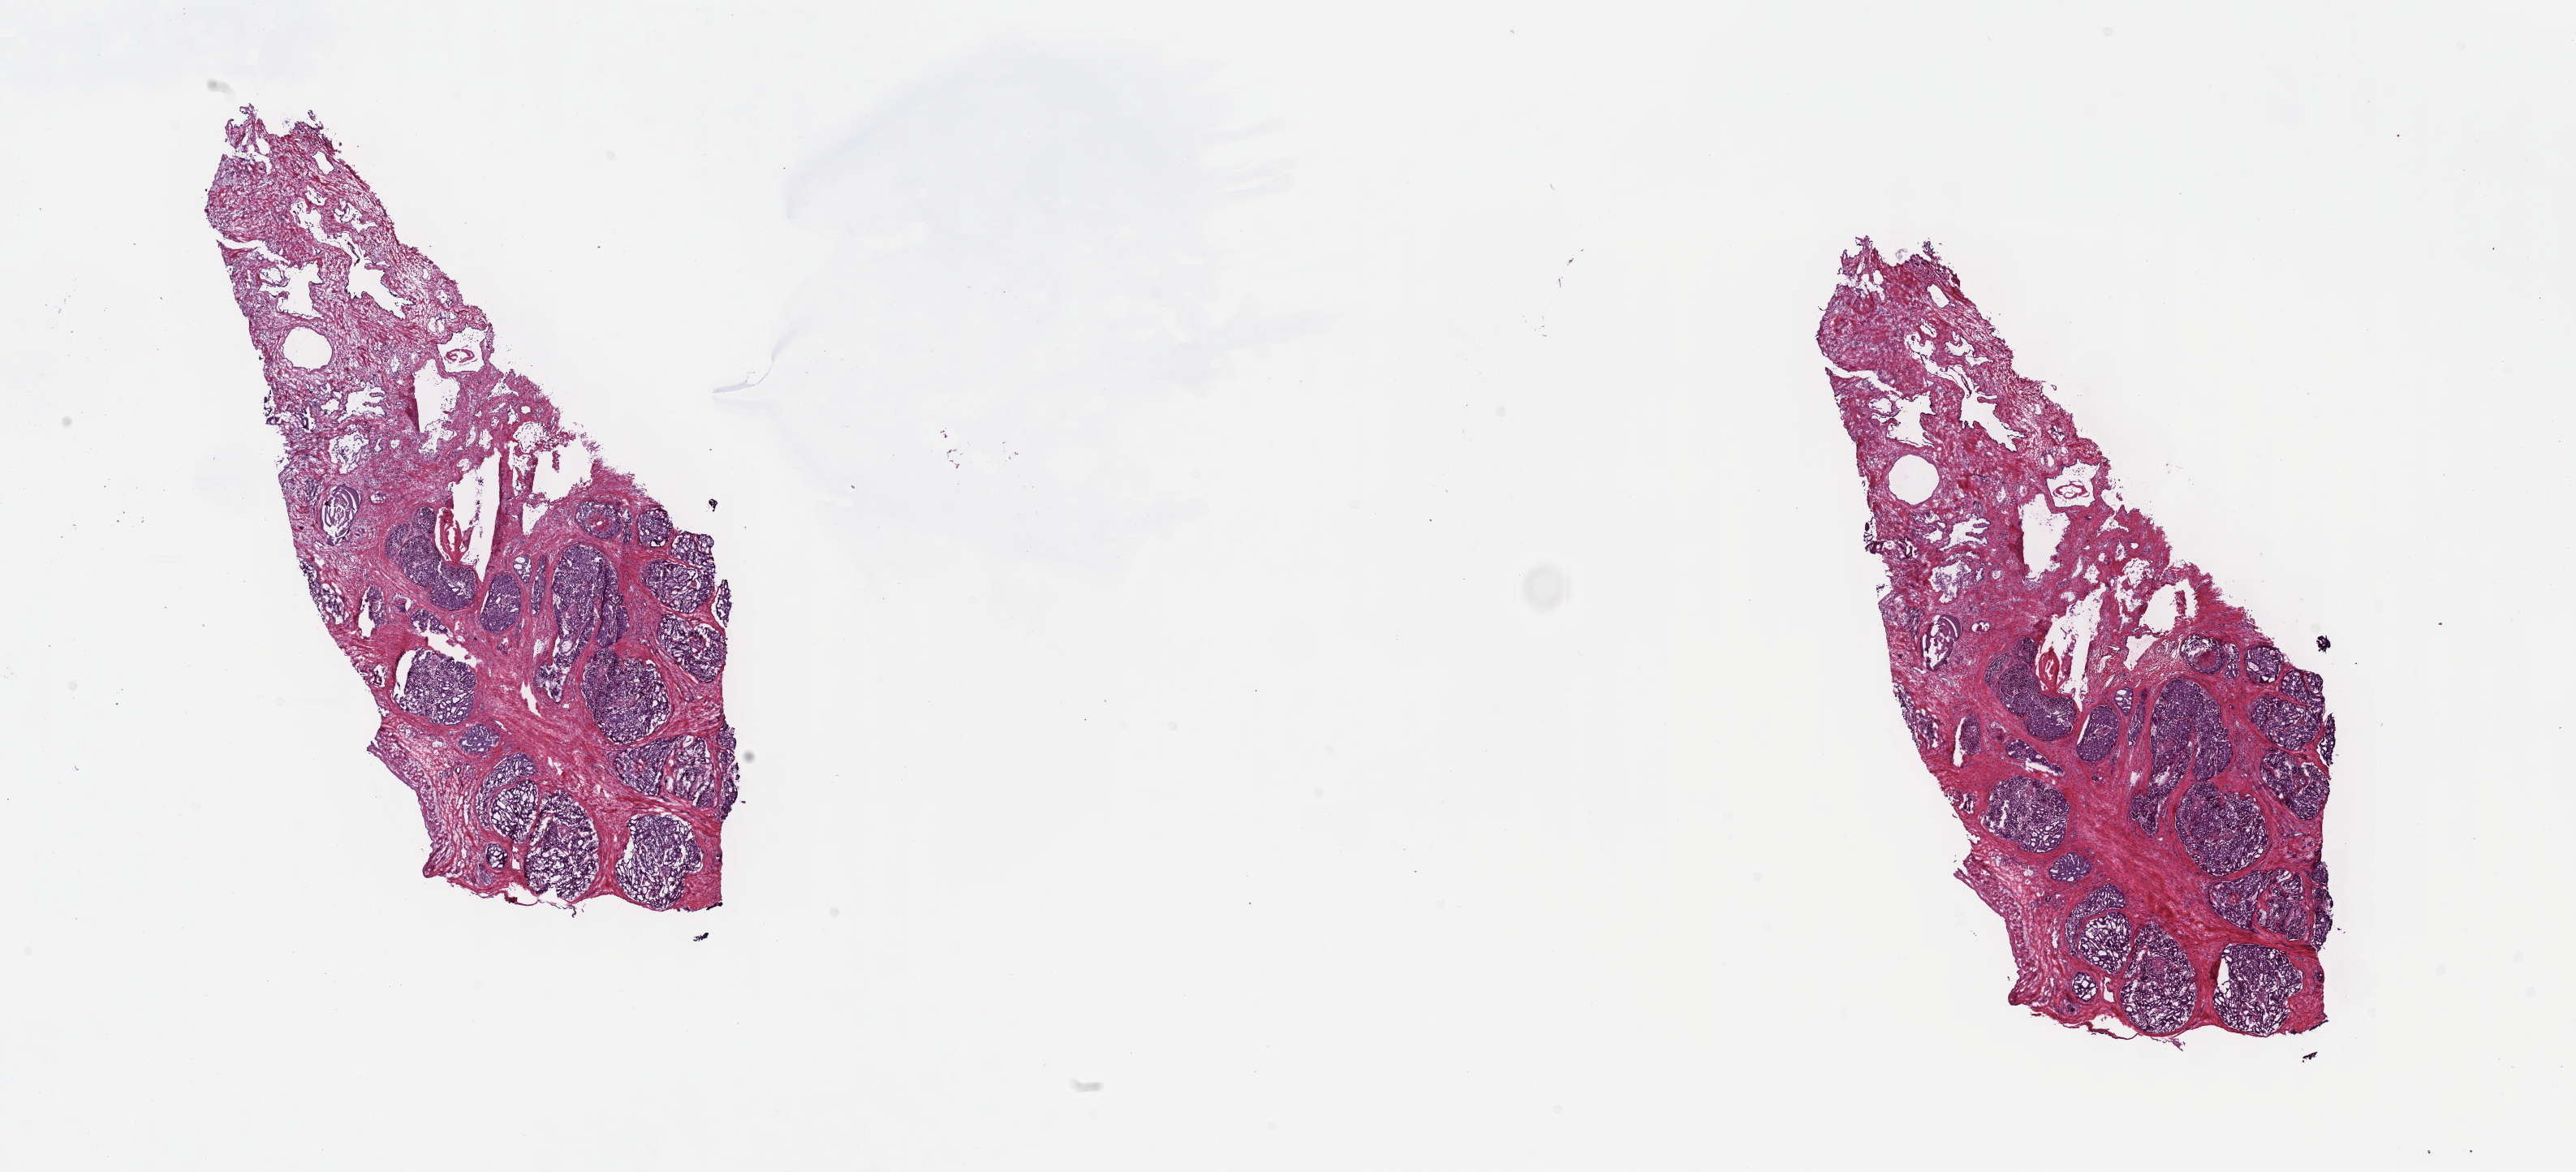
H&E-stained whole-slide image — low-resolution overview of the scanned area, about 25.7 x 11.7 mm; frozen section; prostate, primary tumour sample. Male patient; age at initial diagnosis 59 years. Gleason score: 9 (4+5). Composition of this section per pathologist review: tumour cells 70%, tumour nuclei 70%, normal cells 2%, stromal cells 28%, necrosis 0%. Infiltration values recorded for this section: lymphocyte infiltration 3%, monocyte infiltration 2%, neutrophil infiltration 1%.
Diagnosis: Adenocarcinoma, NOS (prostate gland). Lymph nodes positive (case pathology): 0 of 1 examined.